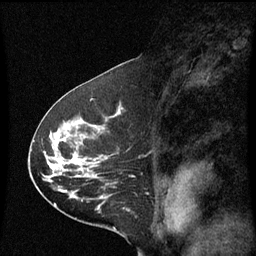
Breast MRI (dynamic contrast-enhanced), one sagittal slice; slice 36 of 60 in the series (ordered by position); dynamic contrast-enhanced series, image 2 of 3 at this slice position (ordered by acquisition); 1.5 T; TE 4.2 ms, TR 8.9 ms; 256 × 256 image matrix, field of view 200 × 200 mm. Female patient, age 53 years. From the clinical record (not read from this slice): setting: breast cancer imaged before/during neoadjuvant chemotherapy; receptor status: HR-positive, HER2-negative.
Structures marked on this image (semi-automatic segmentation, software-assisted and operator-edited):
- analysis volume of interest (the breast-tissue region the enhancement analysis was run in; not a lesion): box from (x=32, y=100) to (x=135, y=221) px
- tumour enhancement mask (voxels above the 70 % enhancement threshold inside the analysis volume of interest): (x=48, y=154)–(x=95, y=195)